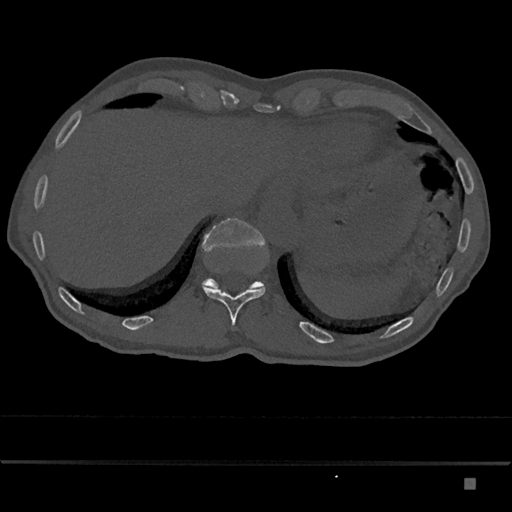
CT including the spine, one axial slice; reconstruction kernel Br40s/3; 120 kVp; bone window (W 1800 / L 400 HU); 0.5 mm slice thickness; 512 × 512 image matrix. Patient: male, 72 years. Case-level facts recorded for this patient, not image findings: primary cancer: prostate.
Outlined on this slice (semi-automatic segmentation, software-assisted and operator-edited):
- T11 vertebra: bounding box (x1, y1, x2, y2) in pixels: (202, 283, 265, 326)
- T12 vertebra: (202, 218, 266, 289)